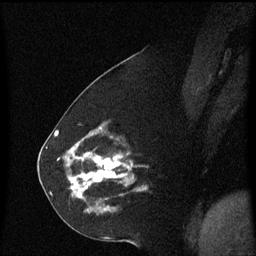
Breast MRI (dynamic contrast-enhanced), one sagittal slice. Slice 26 of 60 in the series (ordered by position). Dynamic contrast-enhanced series, image 2 of 3 at this slice position (ordered by acquisition). 1.5 T. TE 4.2 ms, TR 8.4 ms. 256 × 256 image matrix. Female patient, age 60 years. From the clinical record (not read from this slice): setting: breast cancer imaged before/during neoadjuvant chemotherapy; receptor status: triple-negative.
Structures marked on this image (semi-automatic segmentation, software-assisted and operator-edited):
- analysis volume of interest (the breast-tissue region the enhancement analysis was run in; not a lesion): bounding box (x1, y1, x2, y2) in pixels: (68, 142, 147, 215)
- tumour enhancement mask (voxels above the 70 % enhancement threshold inside the analysis volume of interest): (70, 152, 131, 193)